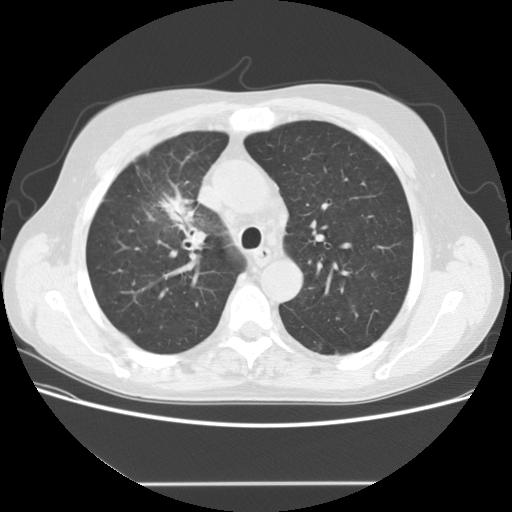
Low-dose screening chest CT, one axial slice; slice 109 of 153 in the series (ordered by position); reconstruction kernel STANDARD; 120 kVp; lung window (W 1500 / L -600 HU); 2.5 mm slice thickness; 512 × 512 image matrix, field of view 360 × 360 mm.
Structures marked on this image (expert manual segmentation):
- lesion 1 (tumor, upper lobe of right lung): bounding box <158,187,195,222> (left, top, right, bottom; pixels)